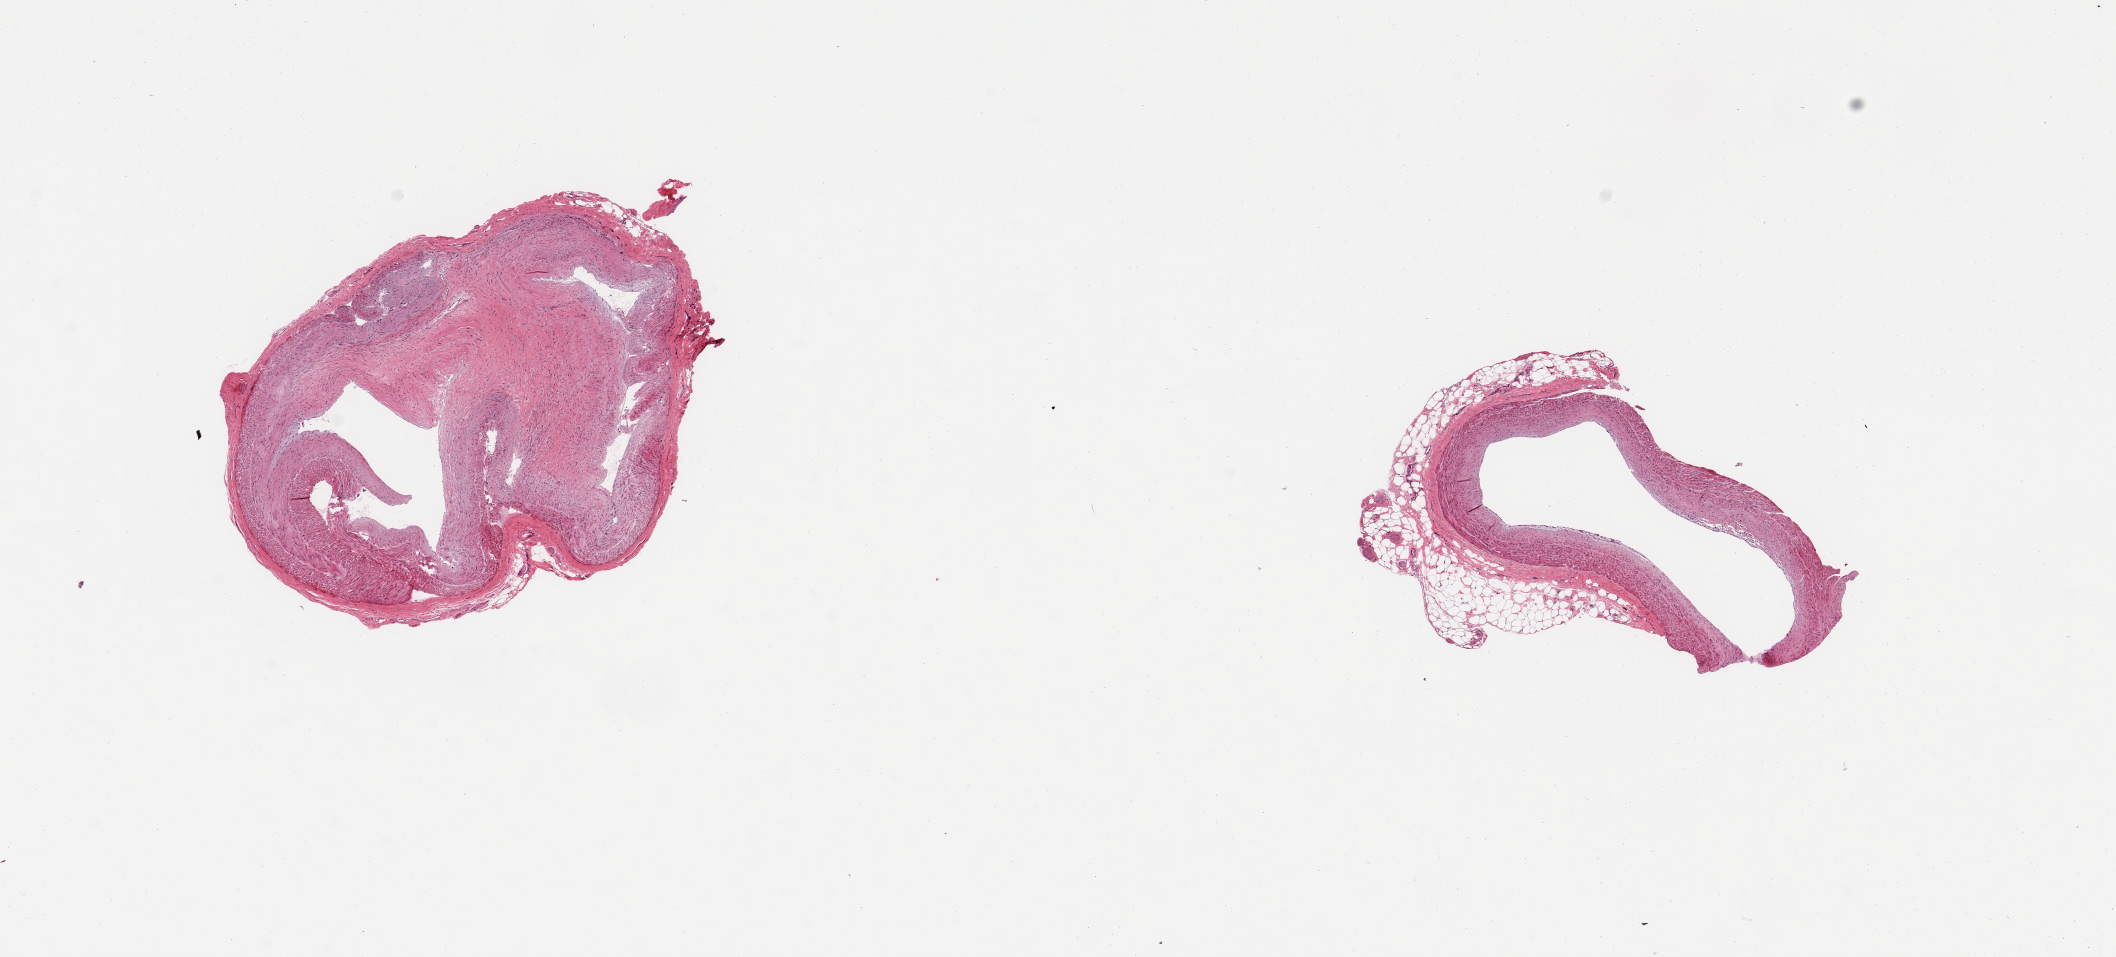
Digitized H&E-stained section, brightfield, whole scanned area (about 16.7 x 7.6 mm, slide scanned at 20x) shown as a low-resolution overview, PAXgene-fixed, paraffin-embedded tissue, section of coronary artery (target tissue), tissue donor sample. Donor sex: male.
• review note (as recorded): 2 pieces, up to 0.7mm rim of adherent fat